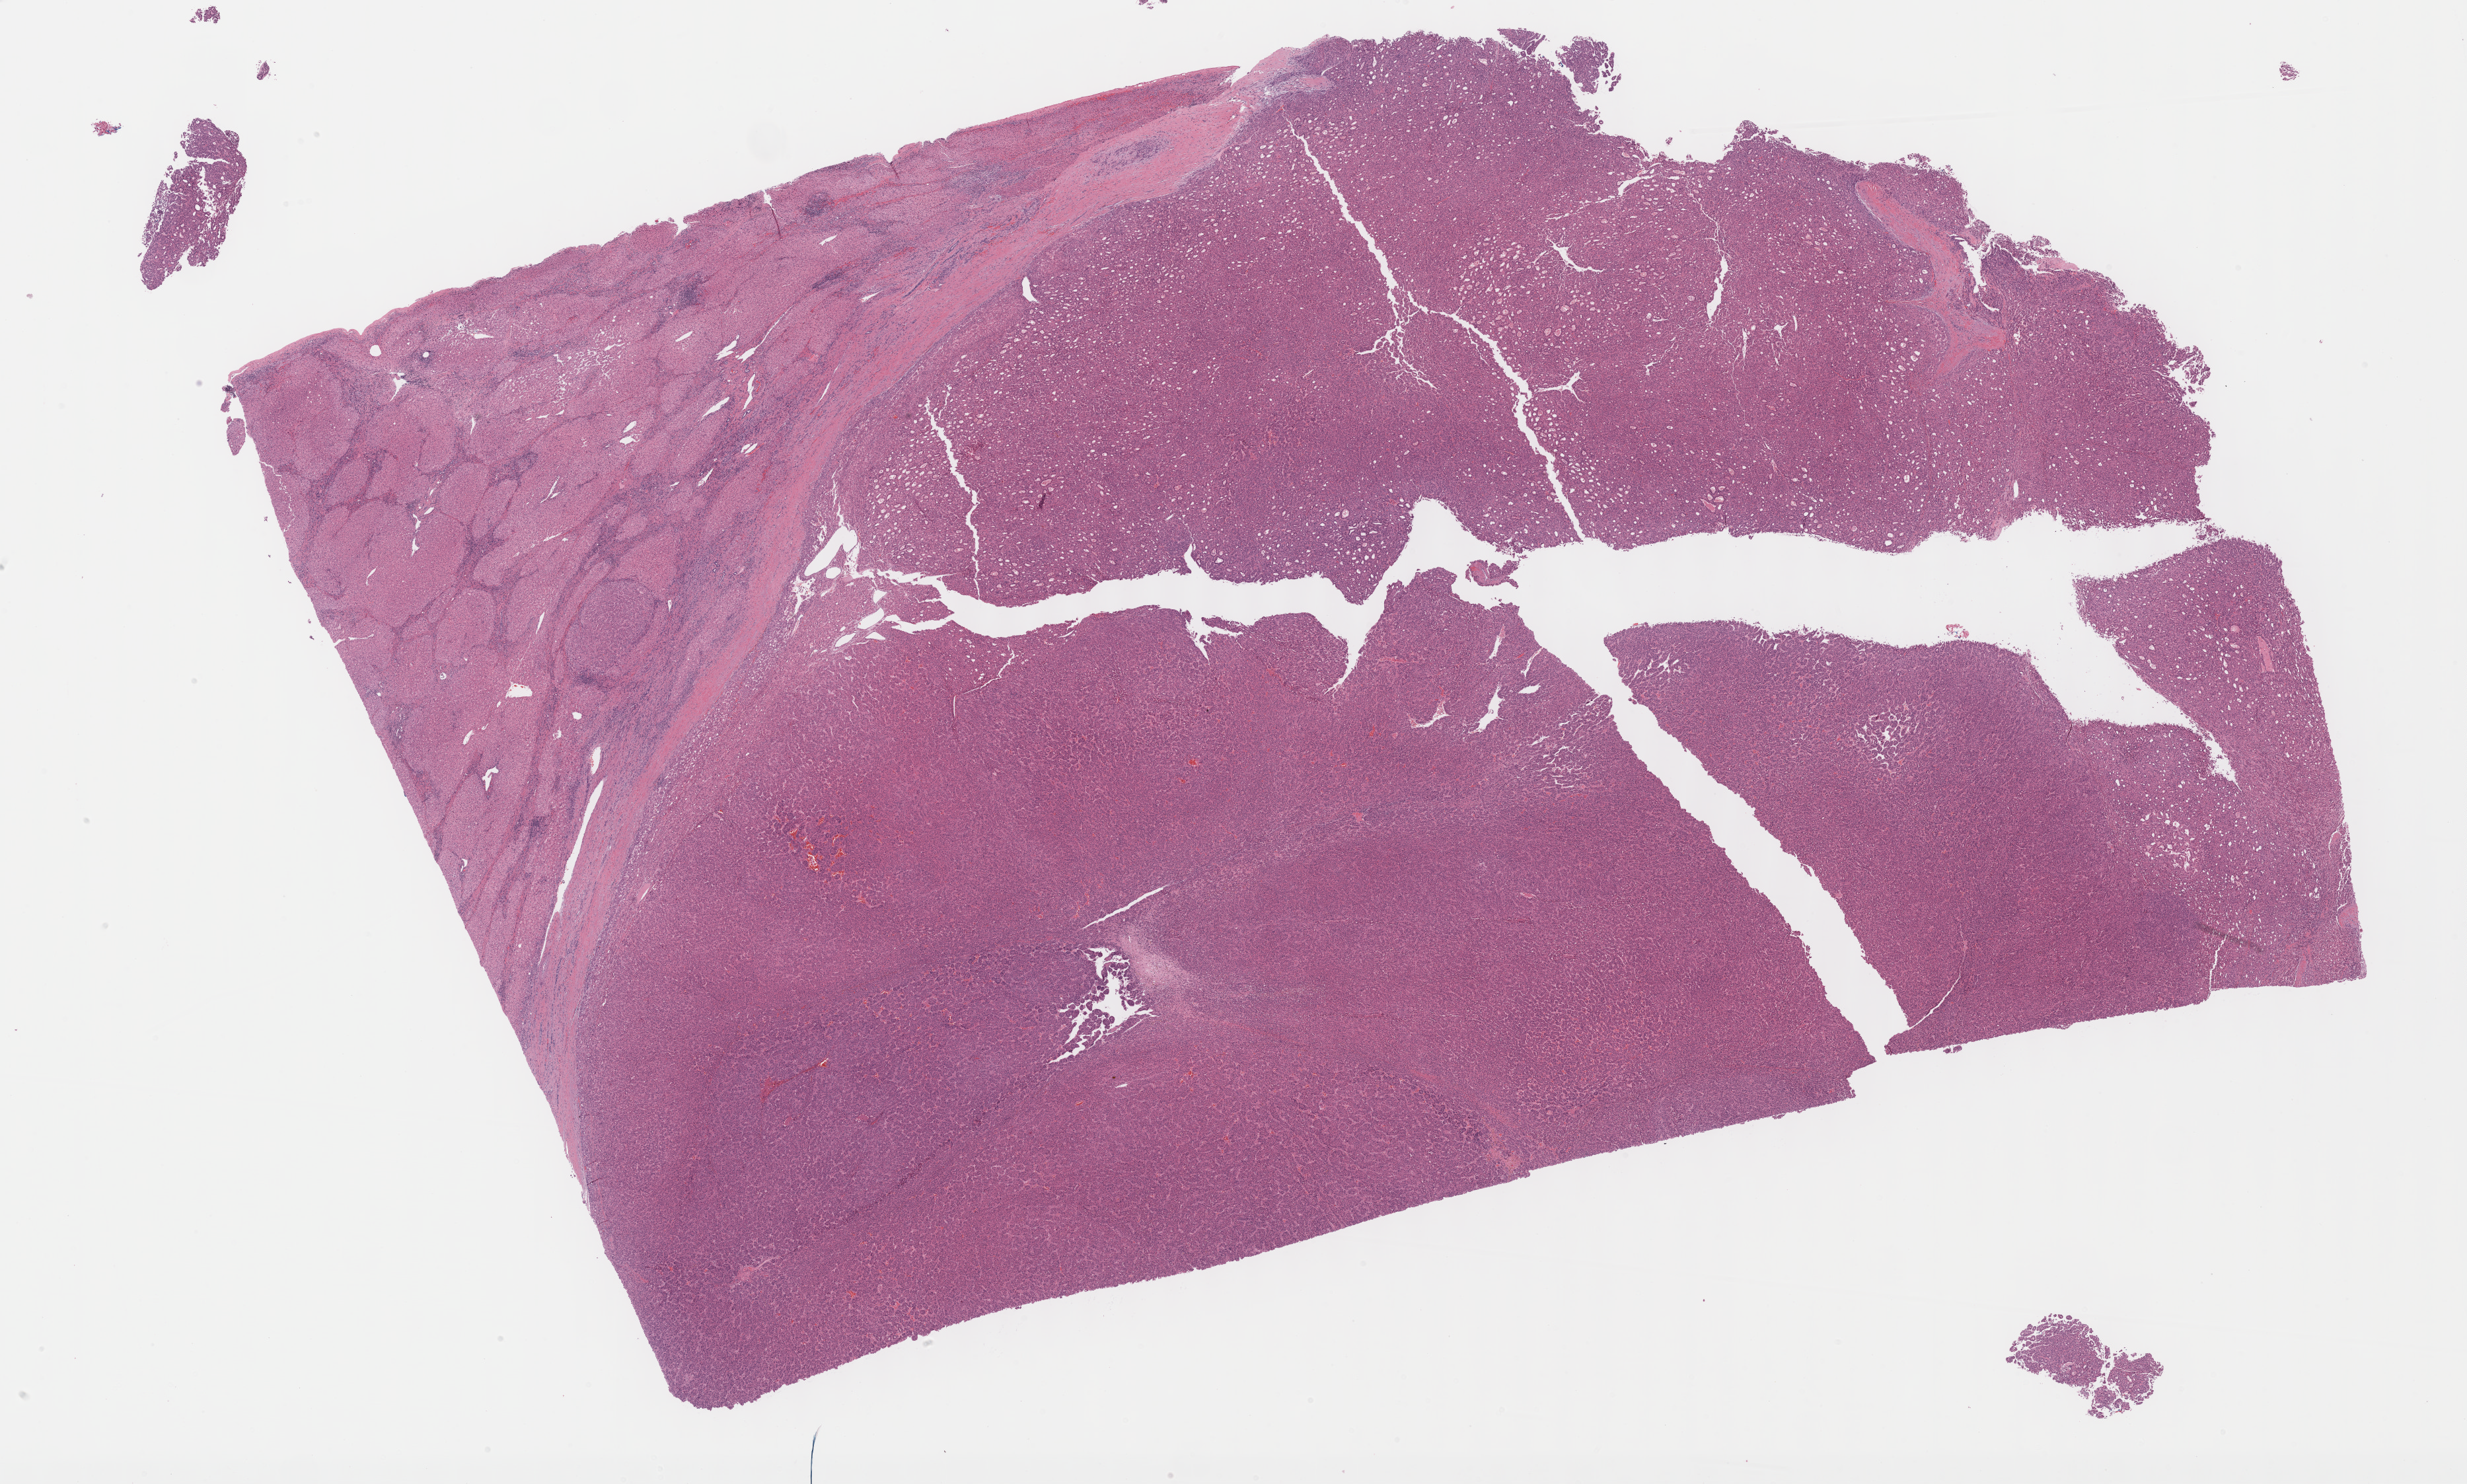
Whole-slide histology image, Hematoxylin and eosin (H&E) stained, a low-resolution overview of the entire scanned area, about 30.2 x 18.2 mm (acquisition: 40x scan), formalin-fixed paraffin-embedded (FFPE) diagnostic section, primary tumour sample from the liver. Patient: male, age at initial diagnosis 65 years. Histologic grade: G2 (moderately differentiated).
- AJCC pathologic stage: IIIB (7th edition)
- histologic diagnosis: Hepatocellular carcinoma, NOS